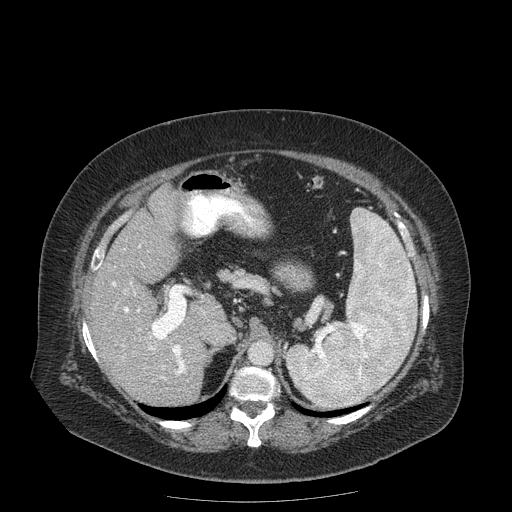
Contrast-enhanced abdominal CT (liver protocol), one axial slice; position 109 of 204 along the scan axis; reconstruction kernel STANDARD; 120 kVp; soft-tissue window (W 400 / L 40 HU); 512 × 512 image matrix, field of view 440 × 440 mm. Case-level facts recorded for this patient, not image findings: diagnosis: hepatocellular carcinoma (patient treated with transarterial chemoembolisation; whether this scan precedes or follows treatment is not stated here); TNM stage (as recorded): Stage-IIIB; Child-Pugh class: A; tumour differentiation: well differentiated.
Annotated regions visible in this slice (semi-automatic segmentation, software-assisted and operator-edited):
- liver parenchyma outside the tumour (the mass and vessels are separate outlines, so this box may not span the whole liver): bounding box [x1, y1, x2, y2] px = [90, 186, 226, 404]
- liver vessels: [99, 245, 186, 380]